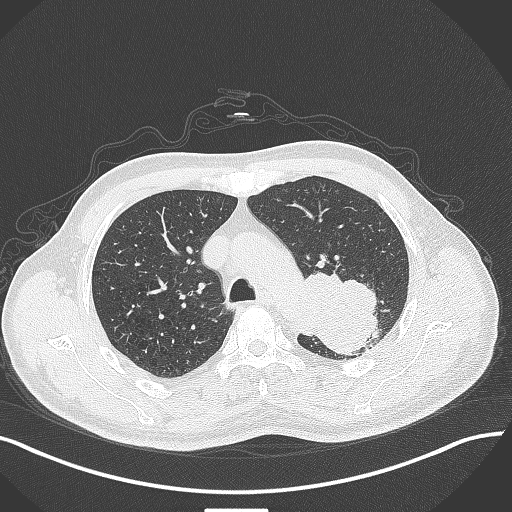
Chest CT, one axial slice. Position 310 of 429 along the scan axis. Reconstruction kernel B70f. 120 kVp. Lung window (W 1500 / L -600 HU). 1 mm slice thickness. 512 × 512 image matrix, field of view 400 × 400 mm. Patient: male, 55 years. From the clinical record (not read from this slice): clinical TNM (as recorded): T3 N0 M1c.
Outlined on this slice (rectangle marked by the reading radiologist):
- lung tumour (recorded histology: adenocarcinoma): bounding box [x1, y1, x2, y2] px = [297, 265, 387, 357]